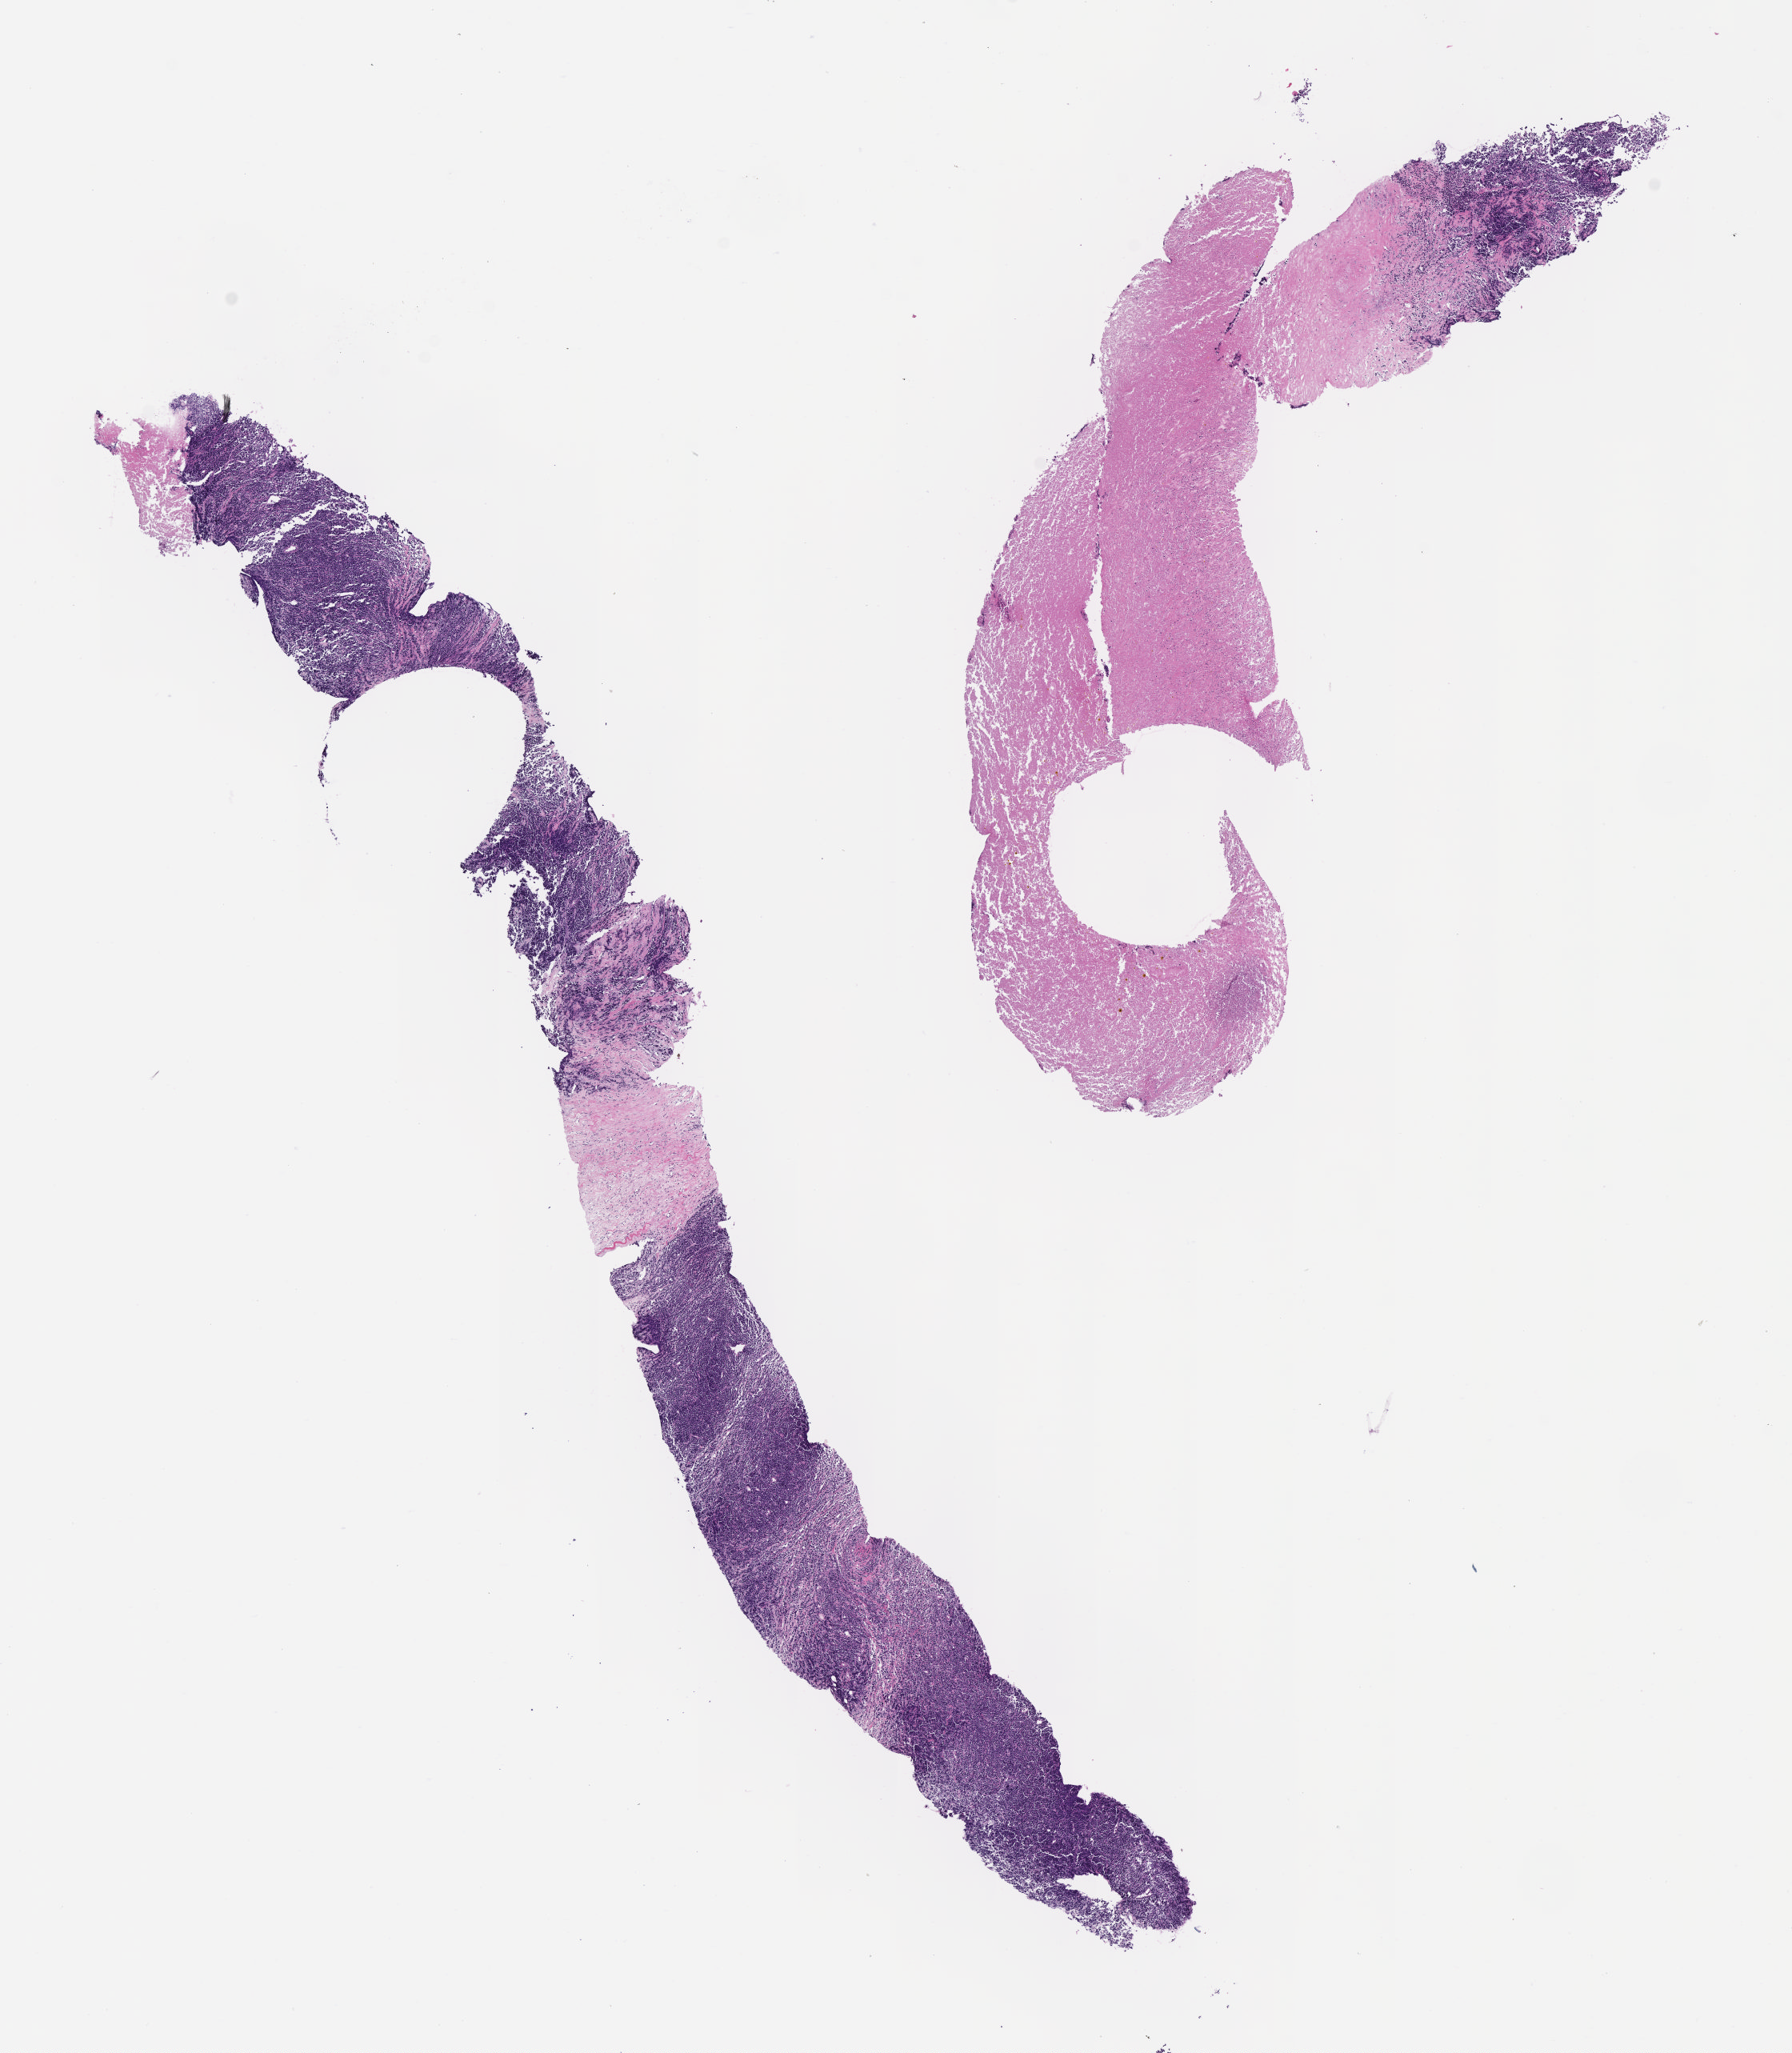
Whole-slide image, hematoxylin and eosin (H&E) stain, shown as a low-resolution overview of the whole scanned area (about 9.1 x 10.4 mm), specimen: tumor tissue. Male patient, 10 years old.
Diagnosis: Burkitt lymphoma, NOS.